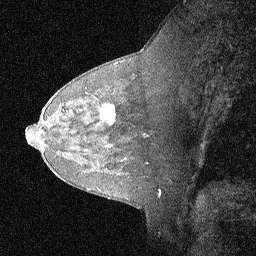
Breast MRI (dynamic contrast-enhanced), one sagittal slice; slice 40 of 64 in the series (ordered by position); dynamic contrast-enhanced study with each time point stored as its own series, time point 2 of 3 at this slice position (early post-contrast, ordered by acquisition time); 1.5 T; TE 4.5 ms, TR 11 ms; 2.06 mm slice thickness; 256 × 256 image matrix, field of view 200 × 200 mm. Female patient, age 62 years. Case-level facts recorded for this patient, not image findings: setting: breast cancer imaged before/during neoadjuvant chemotherapy; receptor status: HR-positive, HER2-negative.
Outlined on this slice (semi-automatic segmentation, software-assisted and operator-edited):
- analysis volume of interest (the breast-tissue region the enhancement analysis was run in; not a lesion): bounding box (x1, y1, x2, y2) in pixels: (91, 93, 124, 129)
- tumour enhancement mask (voxels above the 90 % enhancement threshold inside the analysis volume of interest): (103, 105, 119, 121)